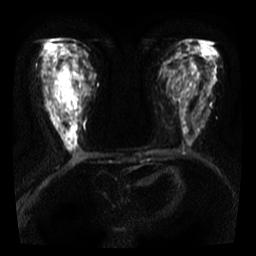
Breast MRI, one axial slice; position 19 of 36 along the scan axis; diffusion-weighted series; image 2 of 4 stored at this slice position (different b-values; order by instance number); 3 T; 5 mm slice thickness; 256 × 256 image matrix, field of view 300 × 300 mm. Female patient.
Outlined on this slice (manually delineated by an expert):
- tumour on diffusion-weighted imaging: box from (x=52, y=68) to (x=75, y=134) px